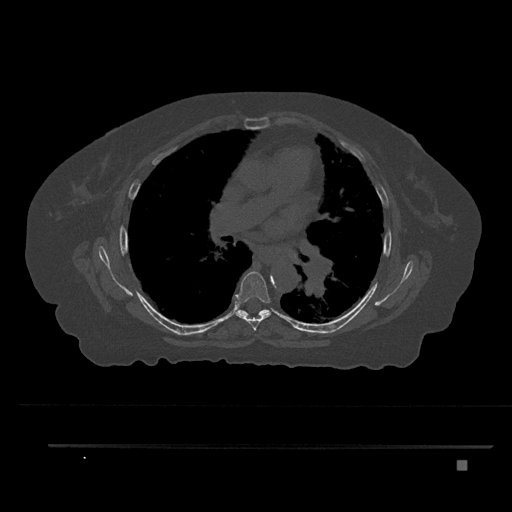
CT including the spine, one axial slice; slice 517 of 797 in the series (ordered by position); bone window (W 1800 / L 400 HU); 0.5 mm slice thickness; 512 × 512 image matrix. Female patient, age 76 years. Case-level facts recorded for this patient, not image findings: primary cancer: lung.
Annotated regions visible in this slice (semi-automatic segmentation, software-assisted and operator-edited):
- T6 vertebra: bounding box (x1, y1, x2, y2) in pixels: (235, 271, 271, 330)
- T7 vertebra: (238, 309, 269, 317)